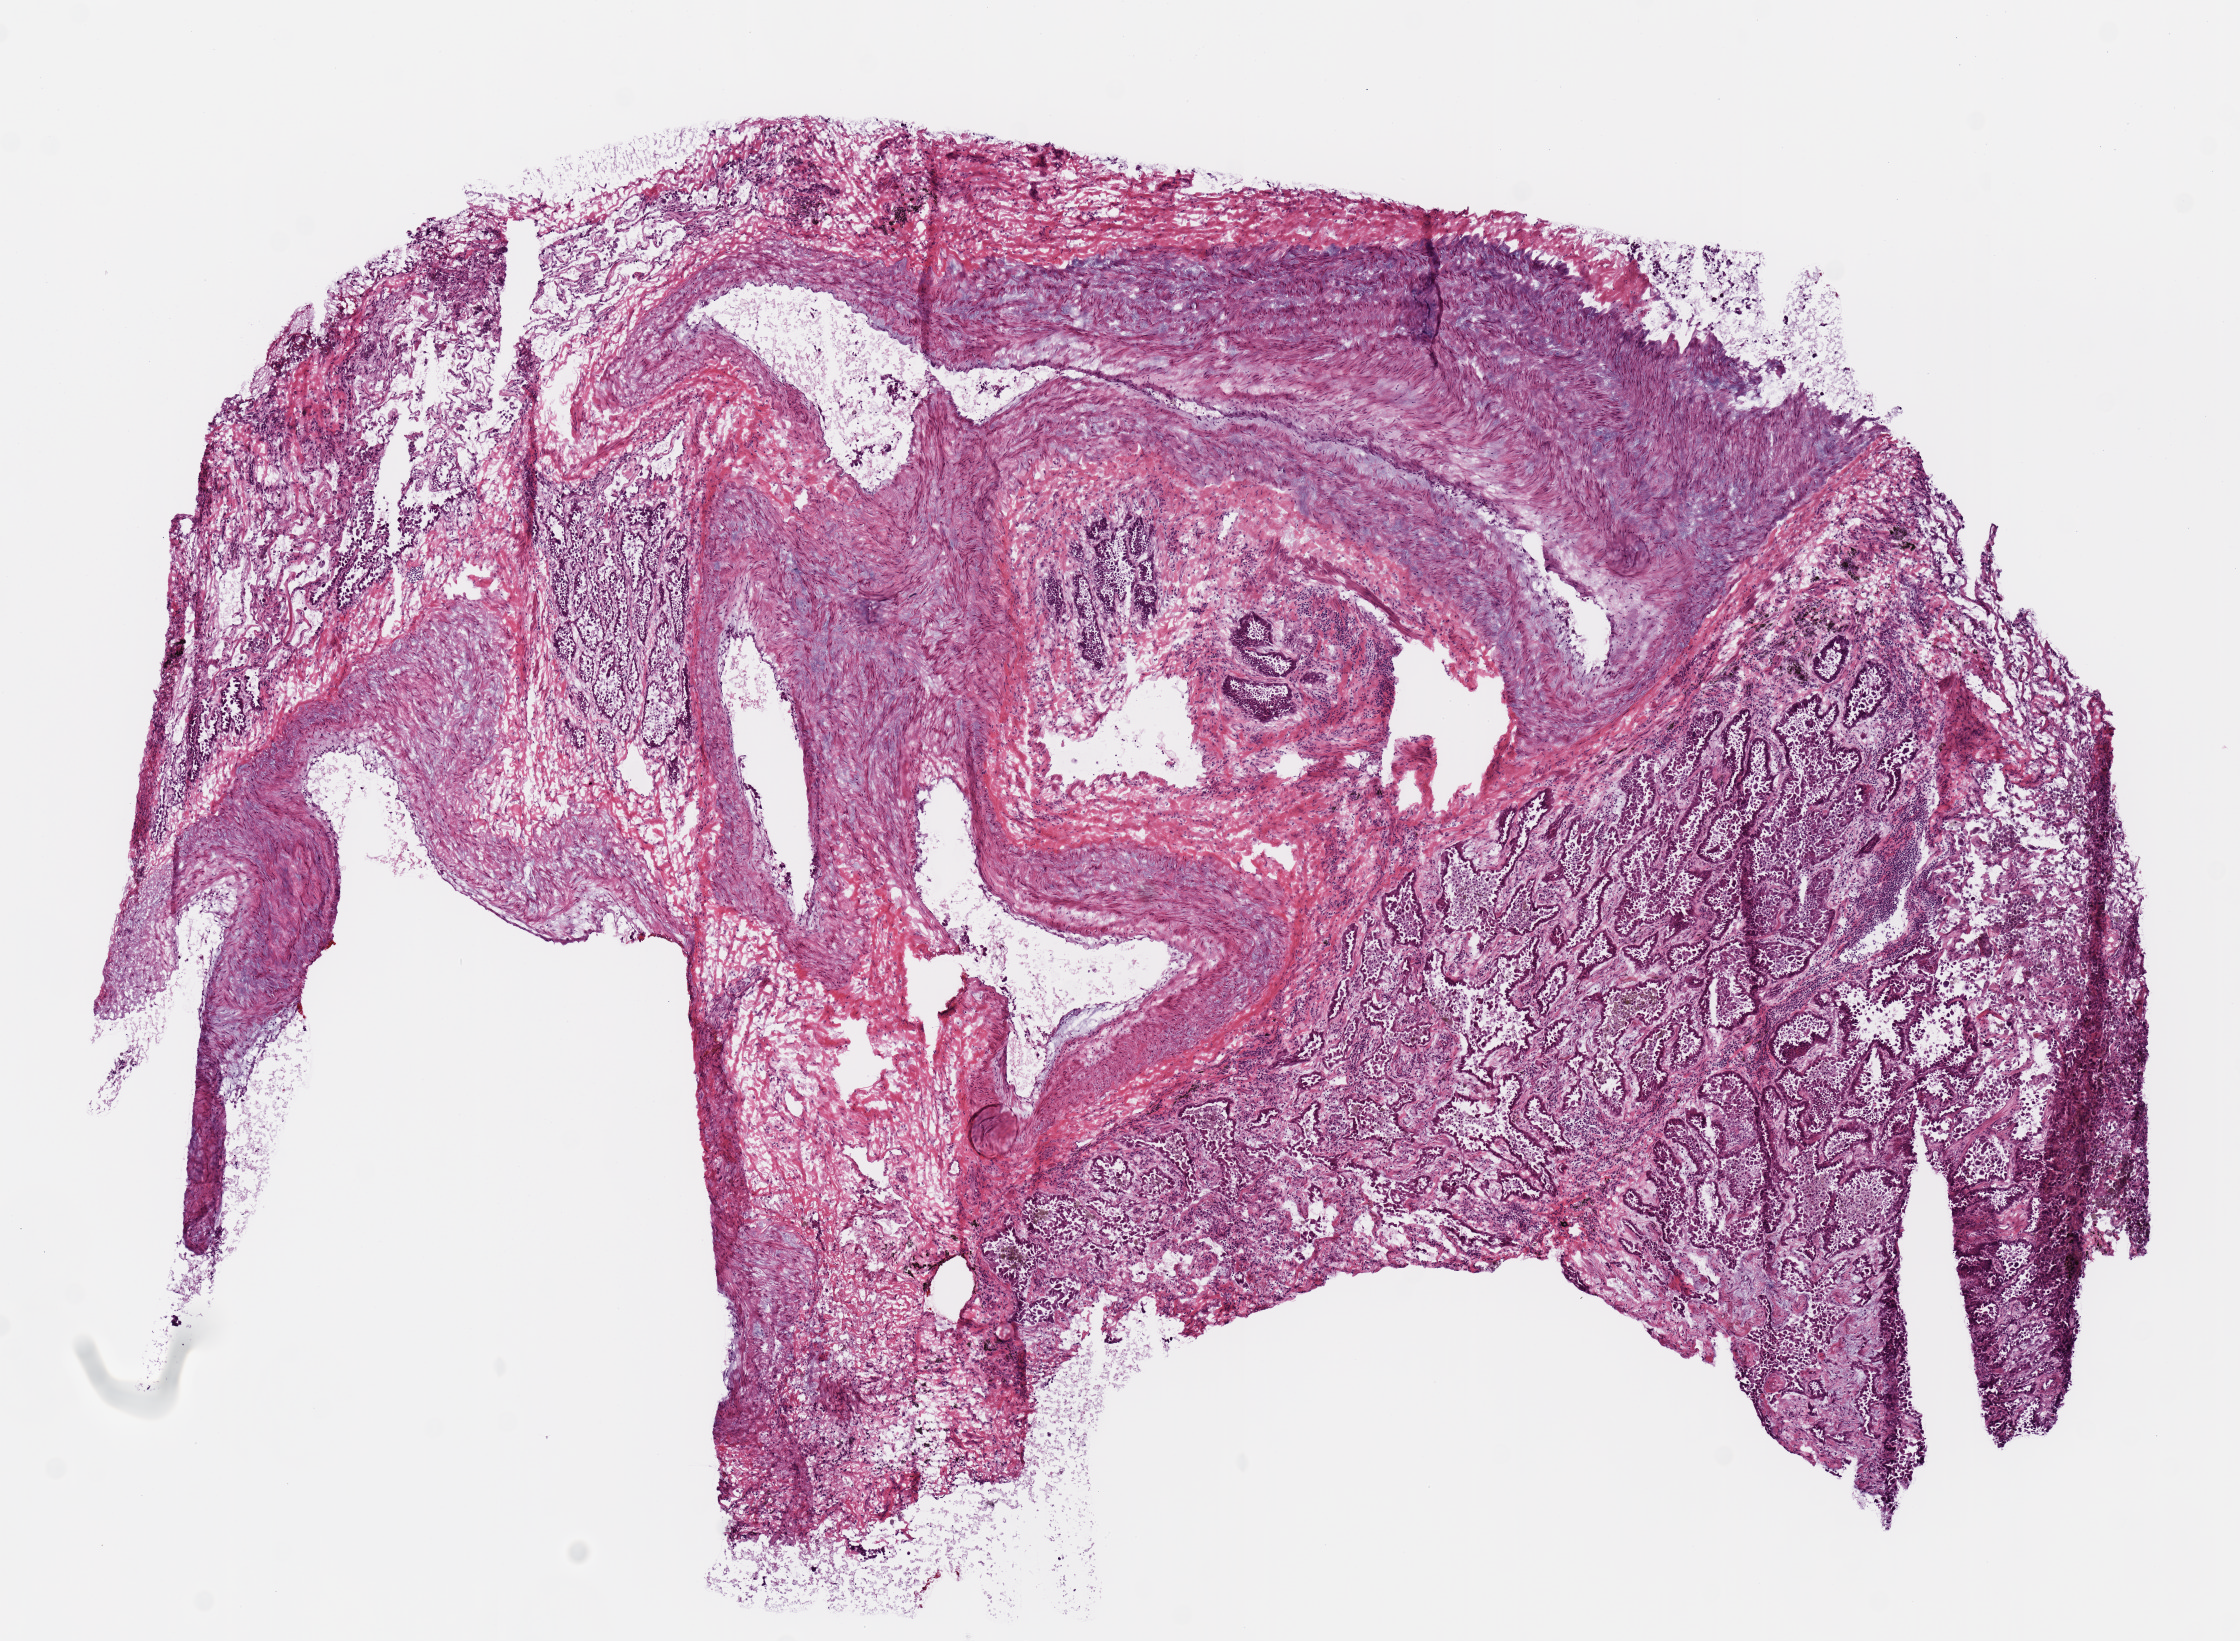
H&E-stained whole-slide image — whole scanned area (about 8.9 x 6.5 mm, slide scanned at 20x) shown as a low-resolution overview, frozen section, sample: primary tumour, lung. Female, age 70 years at initial diagnosis. Slide review estimates, as recorded: tumour cells 85%, tumour nuclei 65%, normal cells 0%, stromal cells 15%, necrosis 0%.
- diagnosis: Adenocarcinoma, NOS (upper lobe, lung)
- AJCC pathologic stage: IB (7th edition)